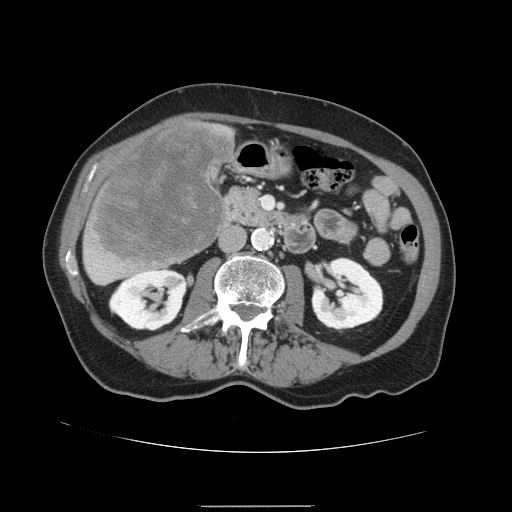
Contrast-enhanced abdominal CT, one axial slice. Slice 49 of 168 in the series (ordered by position). Intravenous contrast given. Soft-tissue window (W 400 / L 40 HU). 2.5 mm slice thickness. 512 × 512 image matrix, field of view 386 × 386 mm. Male patient, age 74 years. Case-level facts recorded for this patient, not image findings: diagnosis: colorectal cancer liver metastases, imaged before liver resection; multiple liver metastases: no; largest metastasis: 14.5 cm; chemotherapy before resection: no.
Structures marked on this image (outlined manually by an expert reader):
- liver: box from (x=82, y=120) to (x=236, y=285) px
- liver metastasis: (x=92, y=125)–(x=234, y=265)